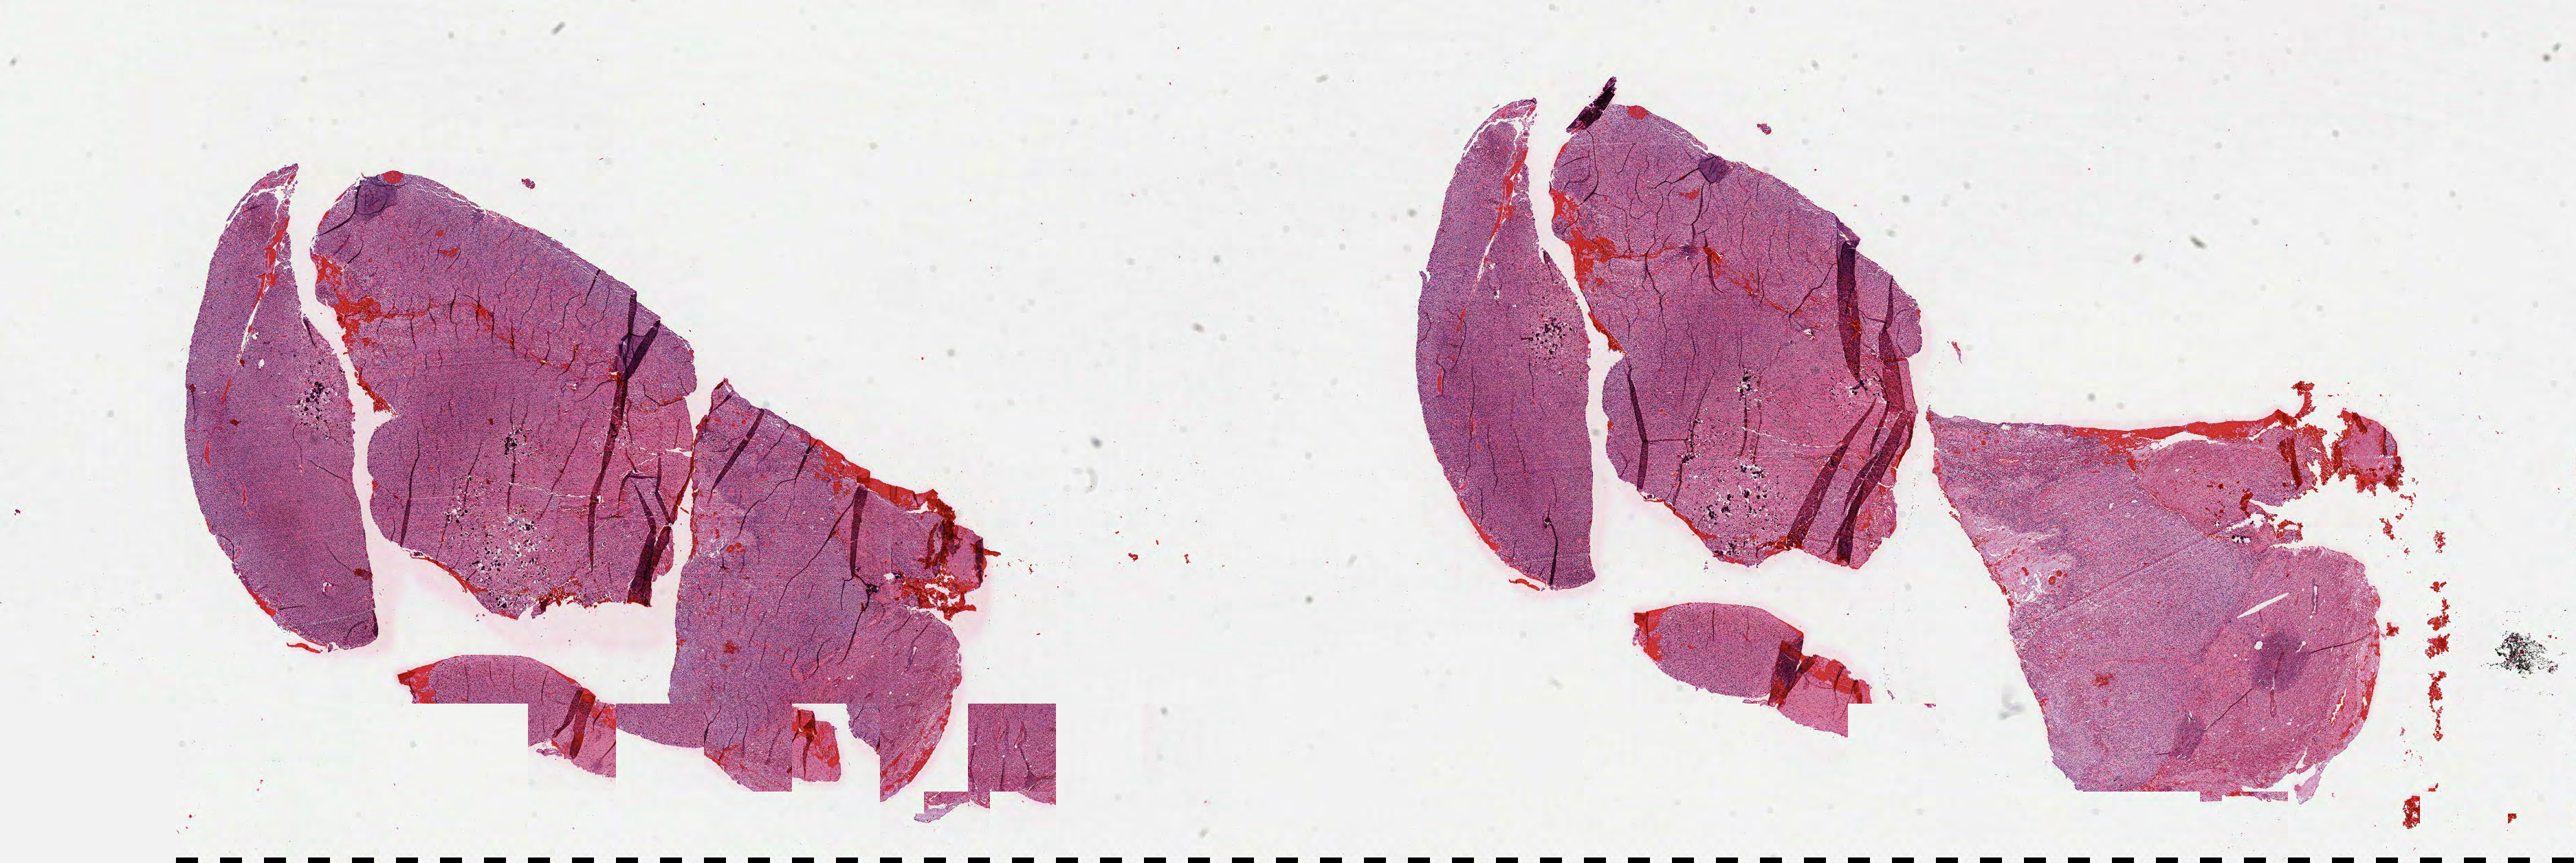
Digitized Hematoxylin and eosin (H&E) stained tissue section (whole slide), shown as a low-resolution overview of the whole scanned area (about 30.2 x 10.1 mm); FFPE section; brain, primary tumour sample. Male patient; age at initial diagnosis 58 years.
Pathologic diagnosis: Mixed glioma.